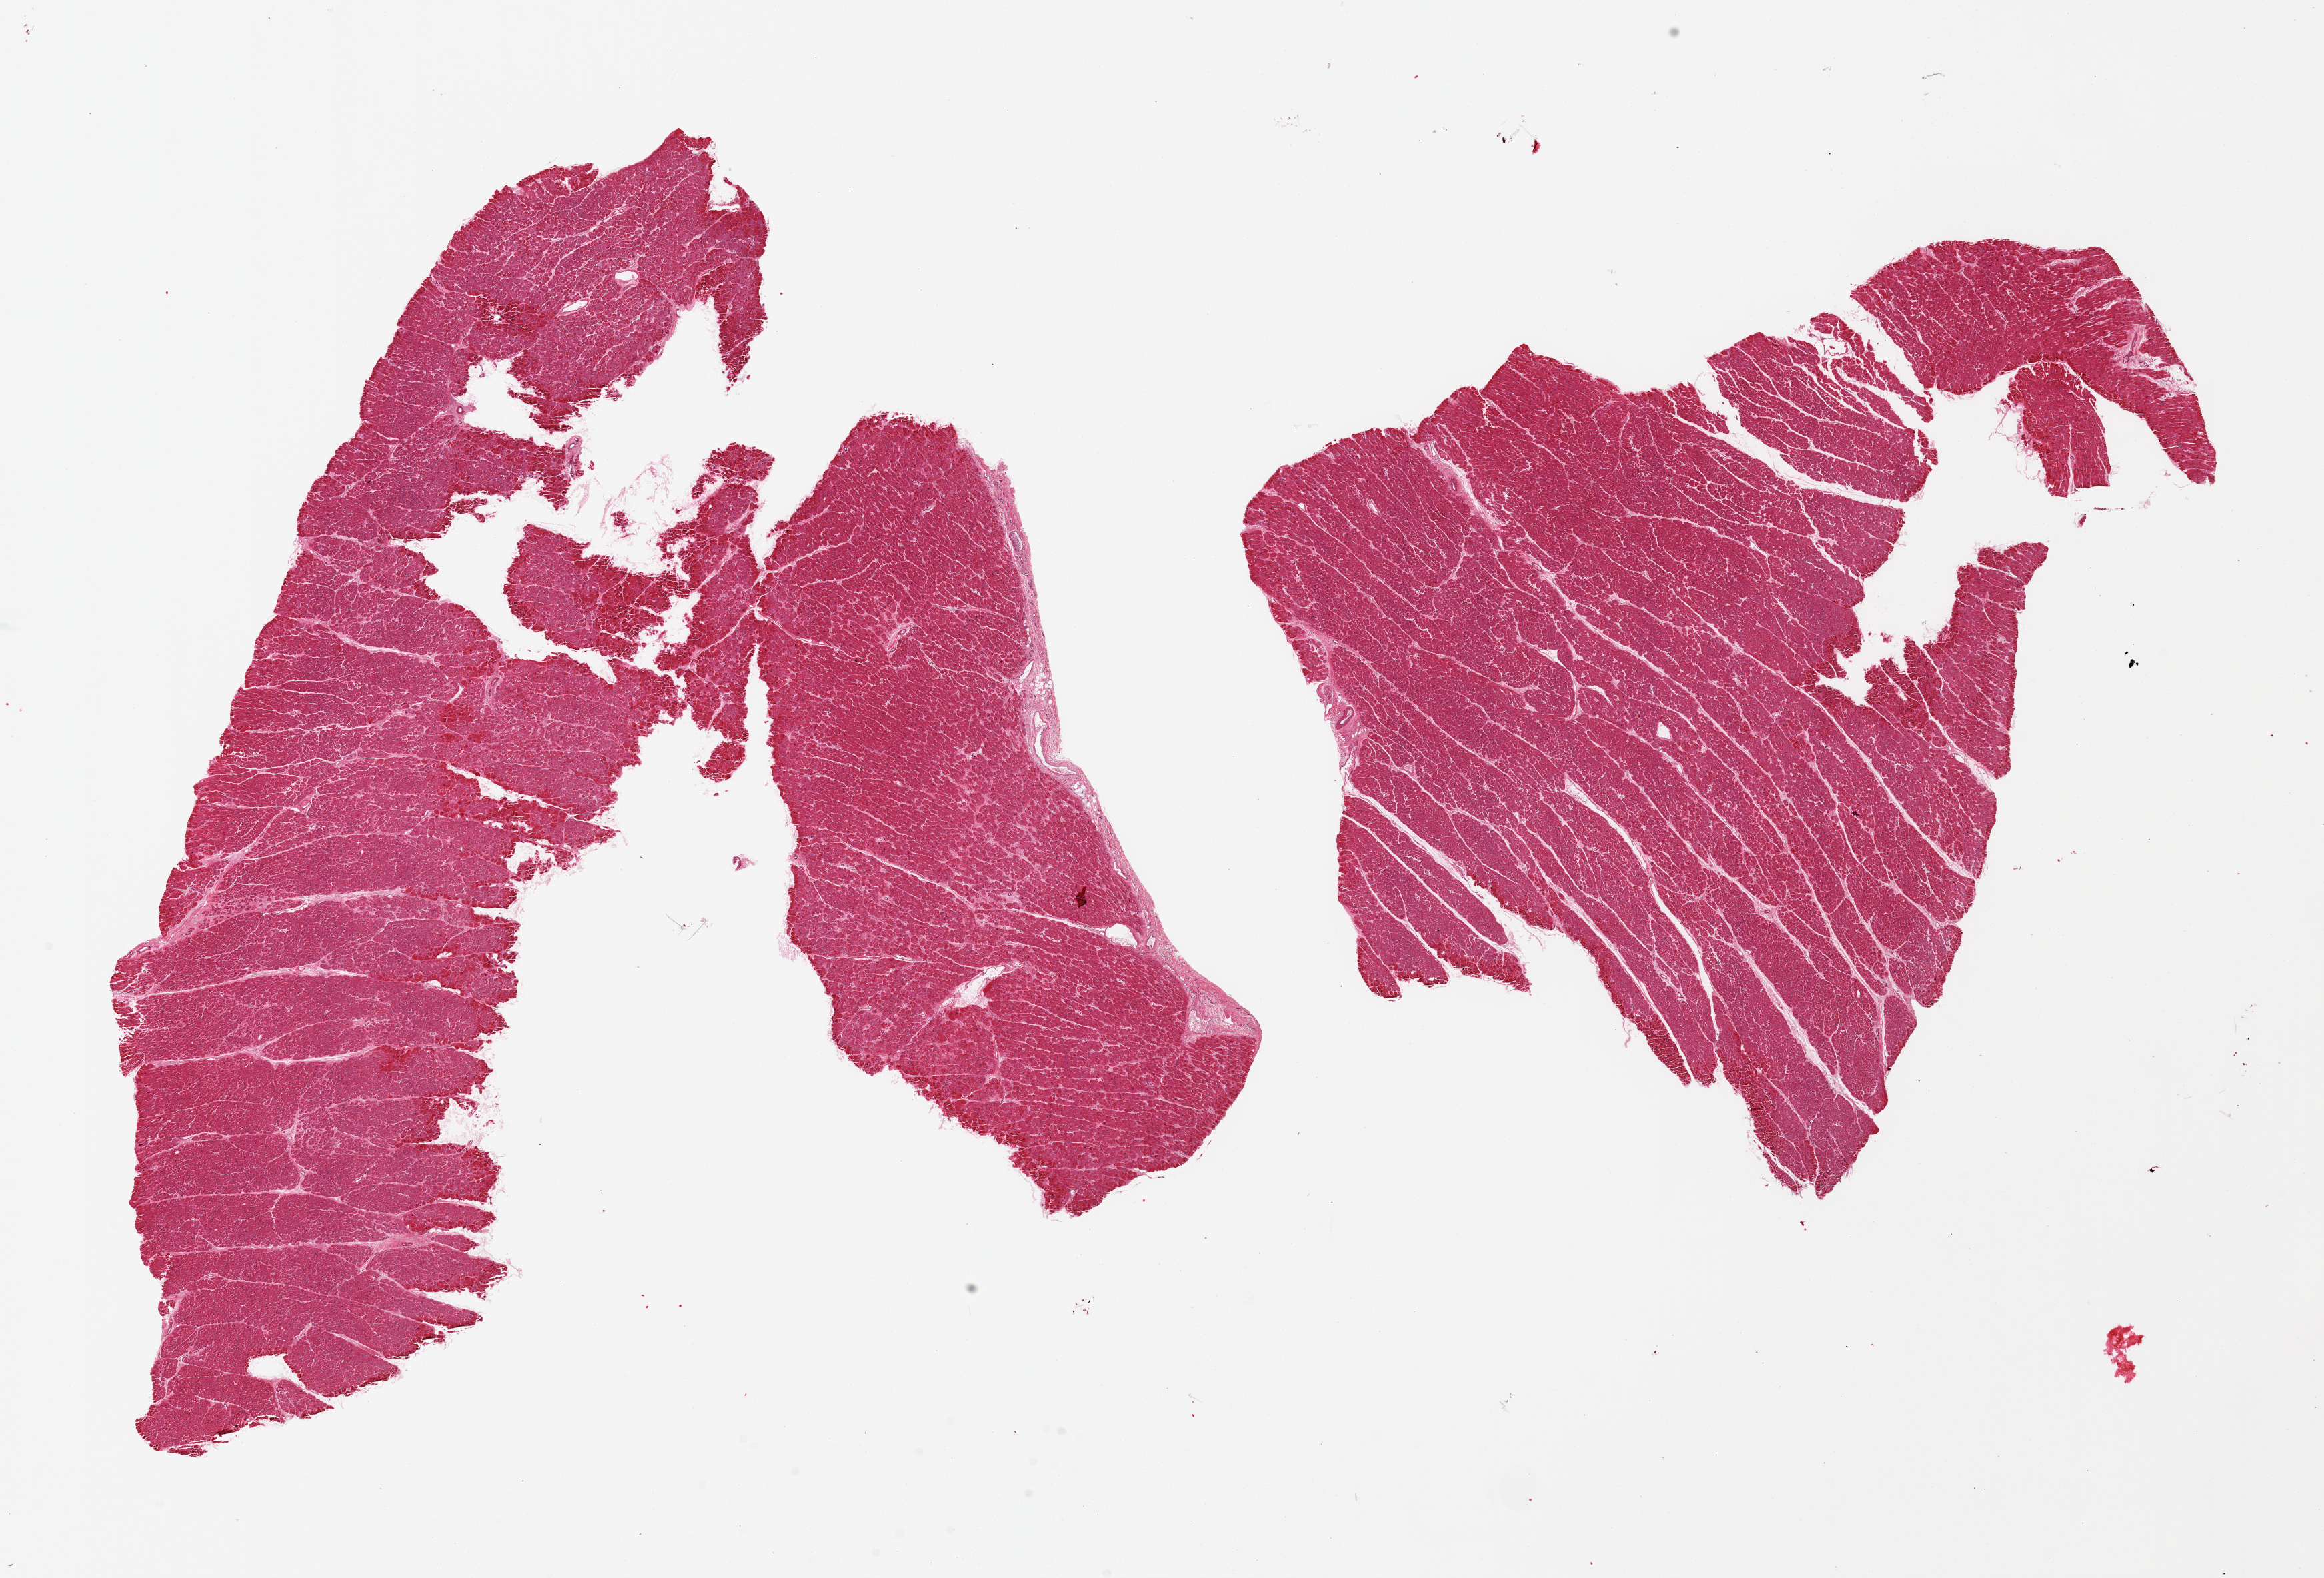
Hematoxylin and eosin (H&E) whole-slide image, low-resolution overview of the scanned area, about 27.6 x 18.7 mm (acquisition: 20x scan); PAXgene-fixed paraffin-embedded (PFPE) section; sampled site (target tissue): heart; tissue donor sample. Donor: male.
* reviewer comment on this tissue sample: 2 pieces. Large nuclei c/w hypertrophy